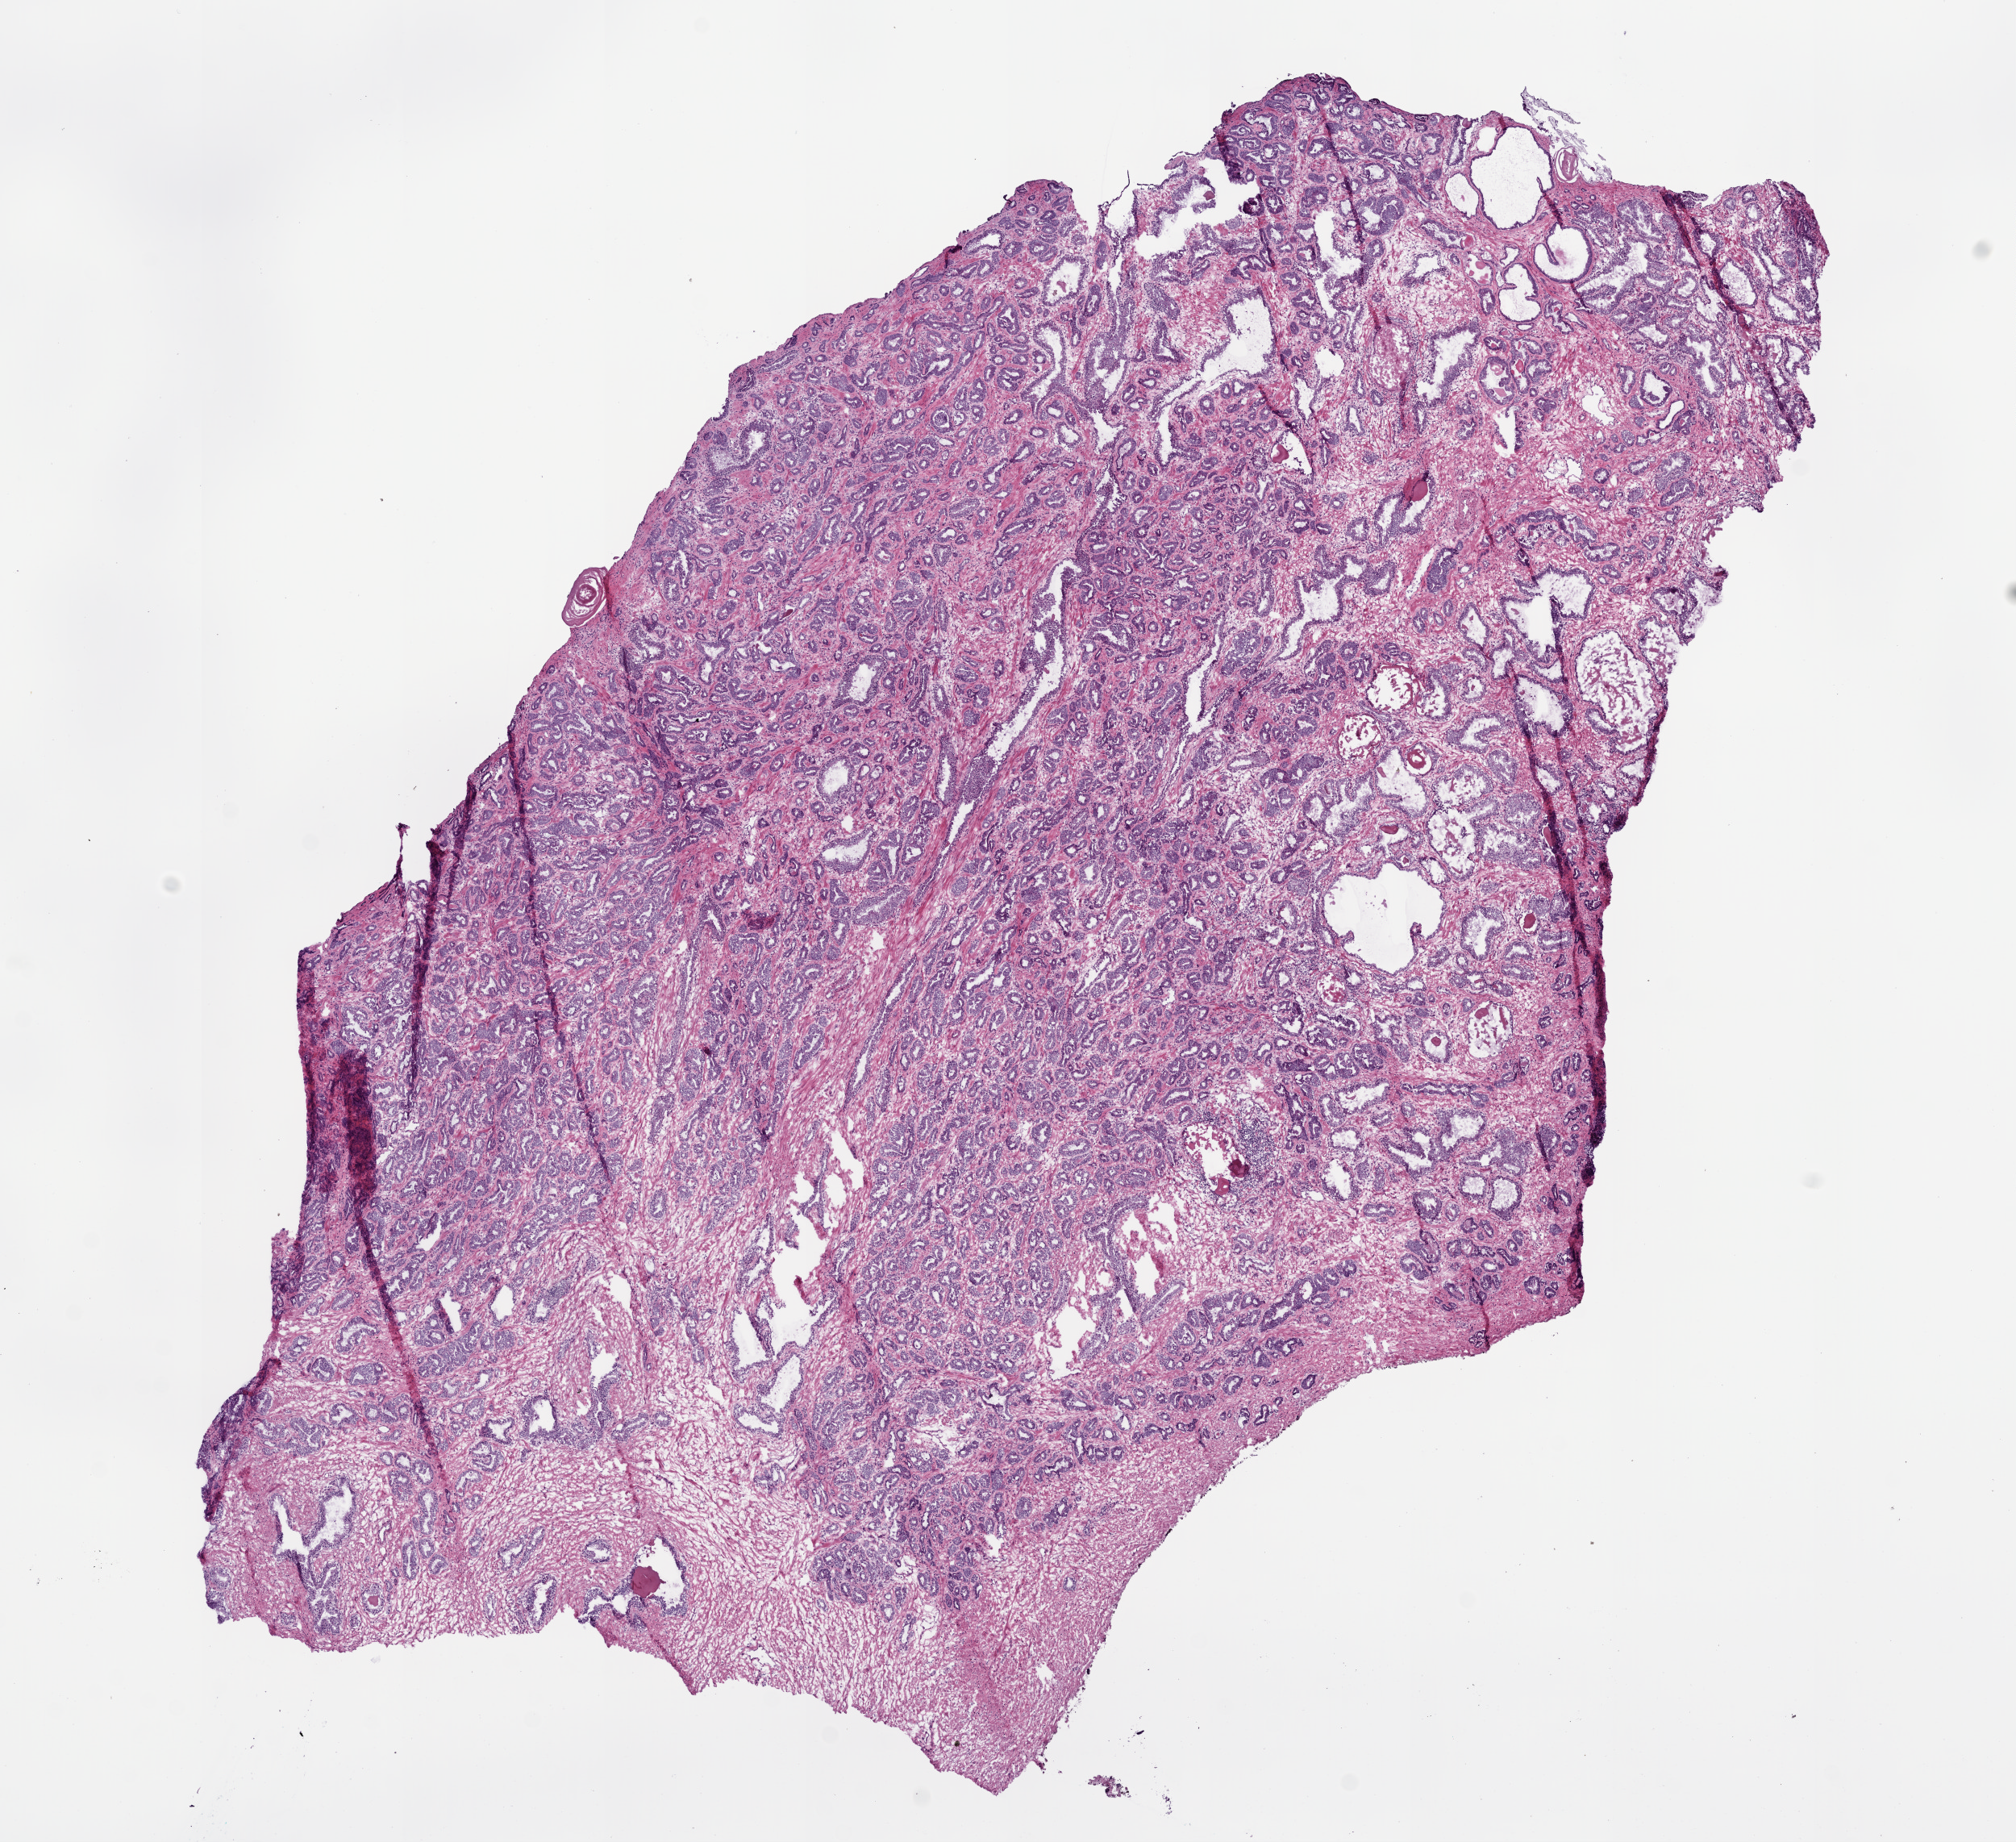
Whole-slide histology image, H&E, whole scanned area (about 10.0 x 9.2 mm) shown as a low-resolution overview. Frozen section. Primary tumour sample from the prostate. Male, age 65 years at initial diagnosis. Gleason score: 7 (3+4). Composition of this section per pathologist review: tumour cells 55%, tumour nuclei 65%, normal cells 20%, stromal cells 25%, necrosis 0%. Inflammatory infiltration, as recorded: lymphocyte infiltration 2%, monocyte infiltration 0%, neutrophil infiltration 0%.
Diagnosis: Acinar cell carcinoma (prostate gland). Laterality: bilateral. Lymph nodes positive (case pathology): 0 of 17 examined.